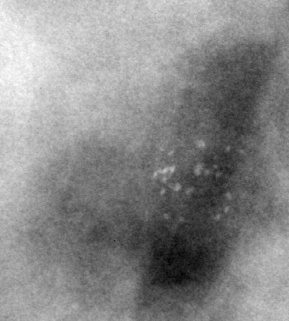
Cropped region of a digitized screen-film mammogram centred on a radiologist-marked abnormality; right breast; MLO view; BI-RADS breast density category 4 (scale 1–4).
Calcifications, morphology punctate / pleomorphic, distribution clustered; BI-RADS assessment category 4; pathology (as recorded): benign.